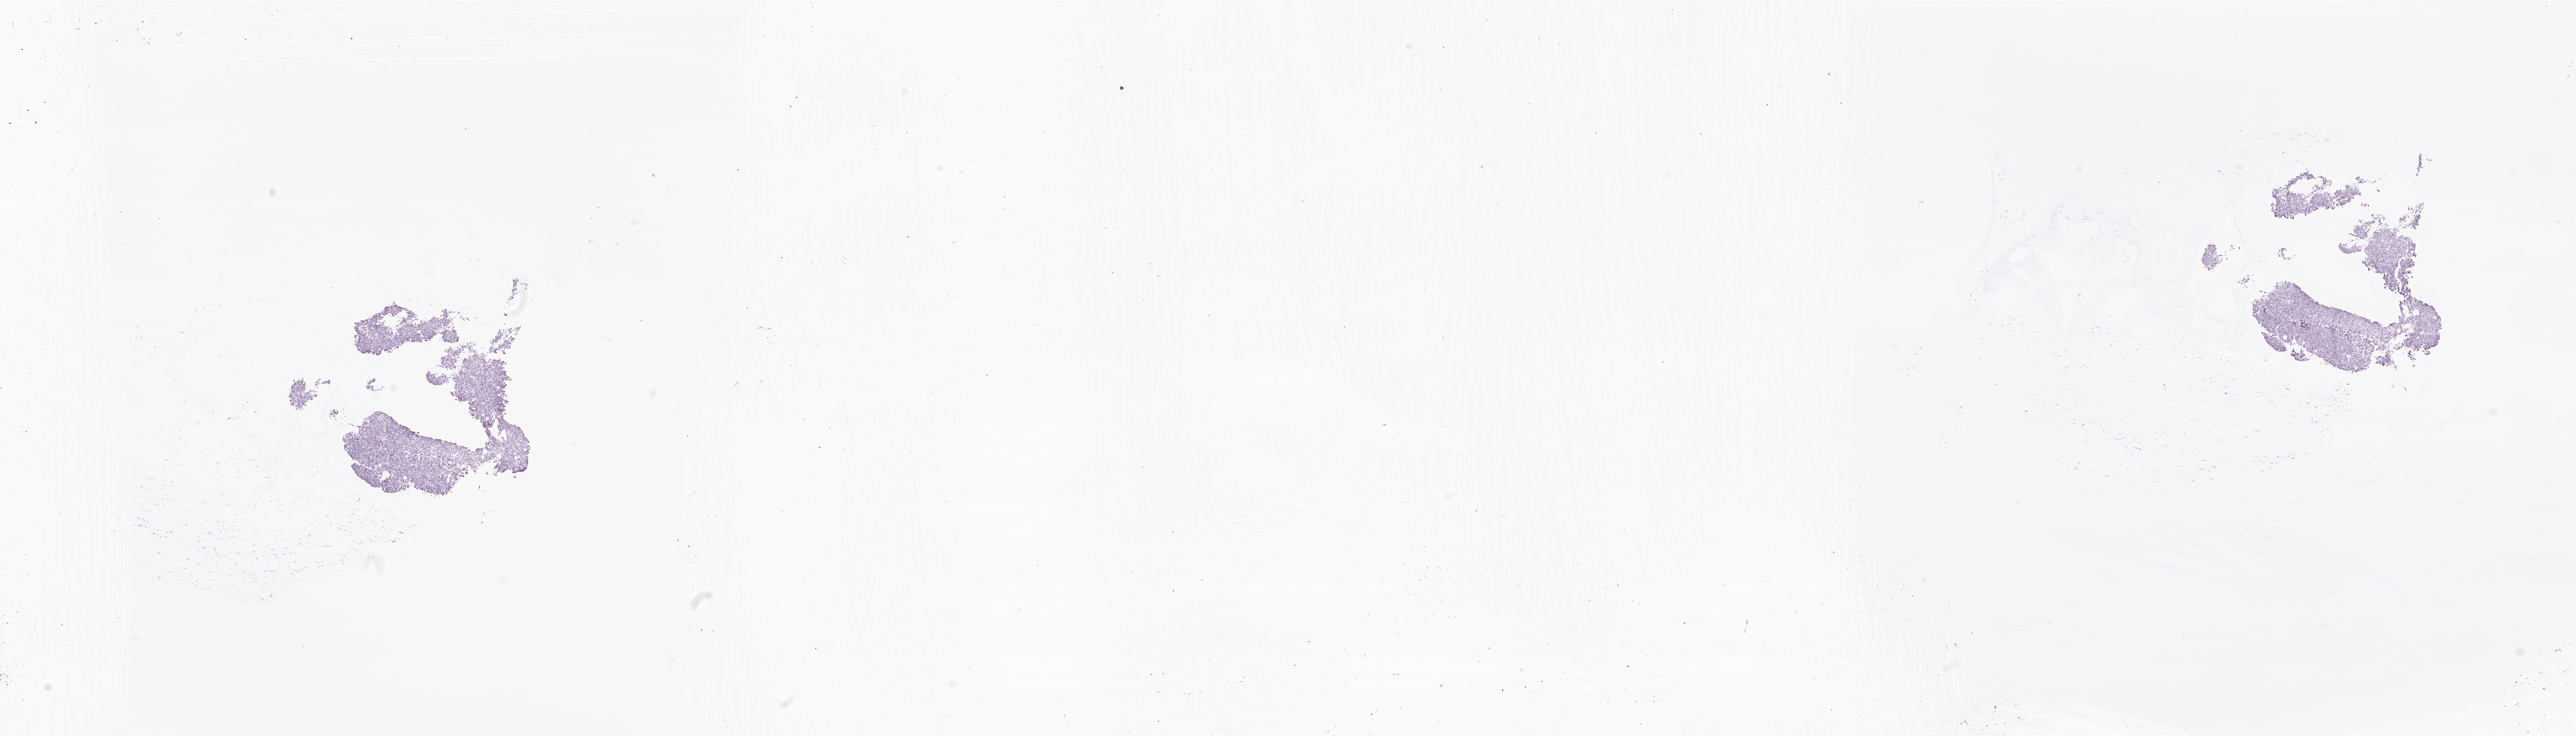
Digitized haematoxylin and eosin-stained section of tumor tissue from the brain, shown as a low-resolution overview of the whole scanned area (about 35.9 x 10.2 mm). Cryosection (OCT / tissue freezing medium). Patient female; age 144 months.
Recorded diagnosis: Medulloblastoma, NOS.